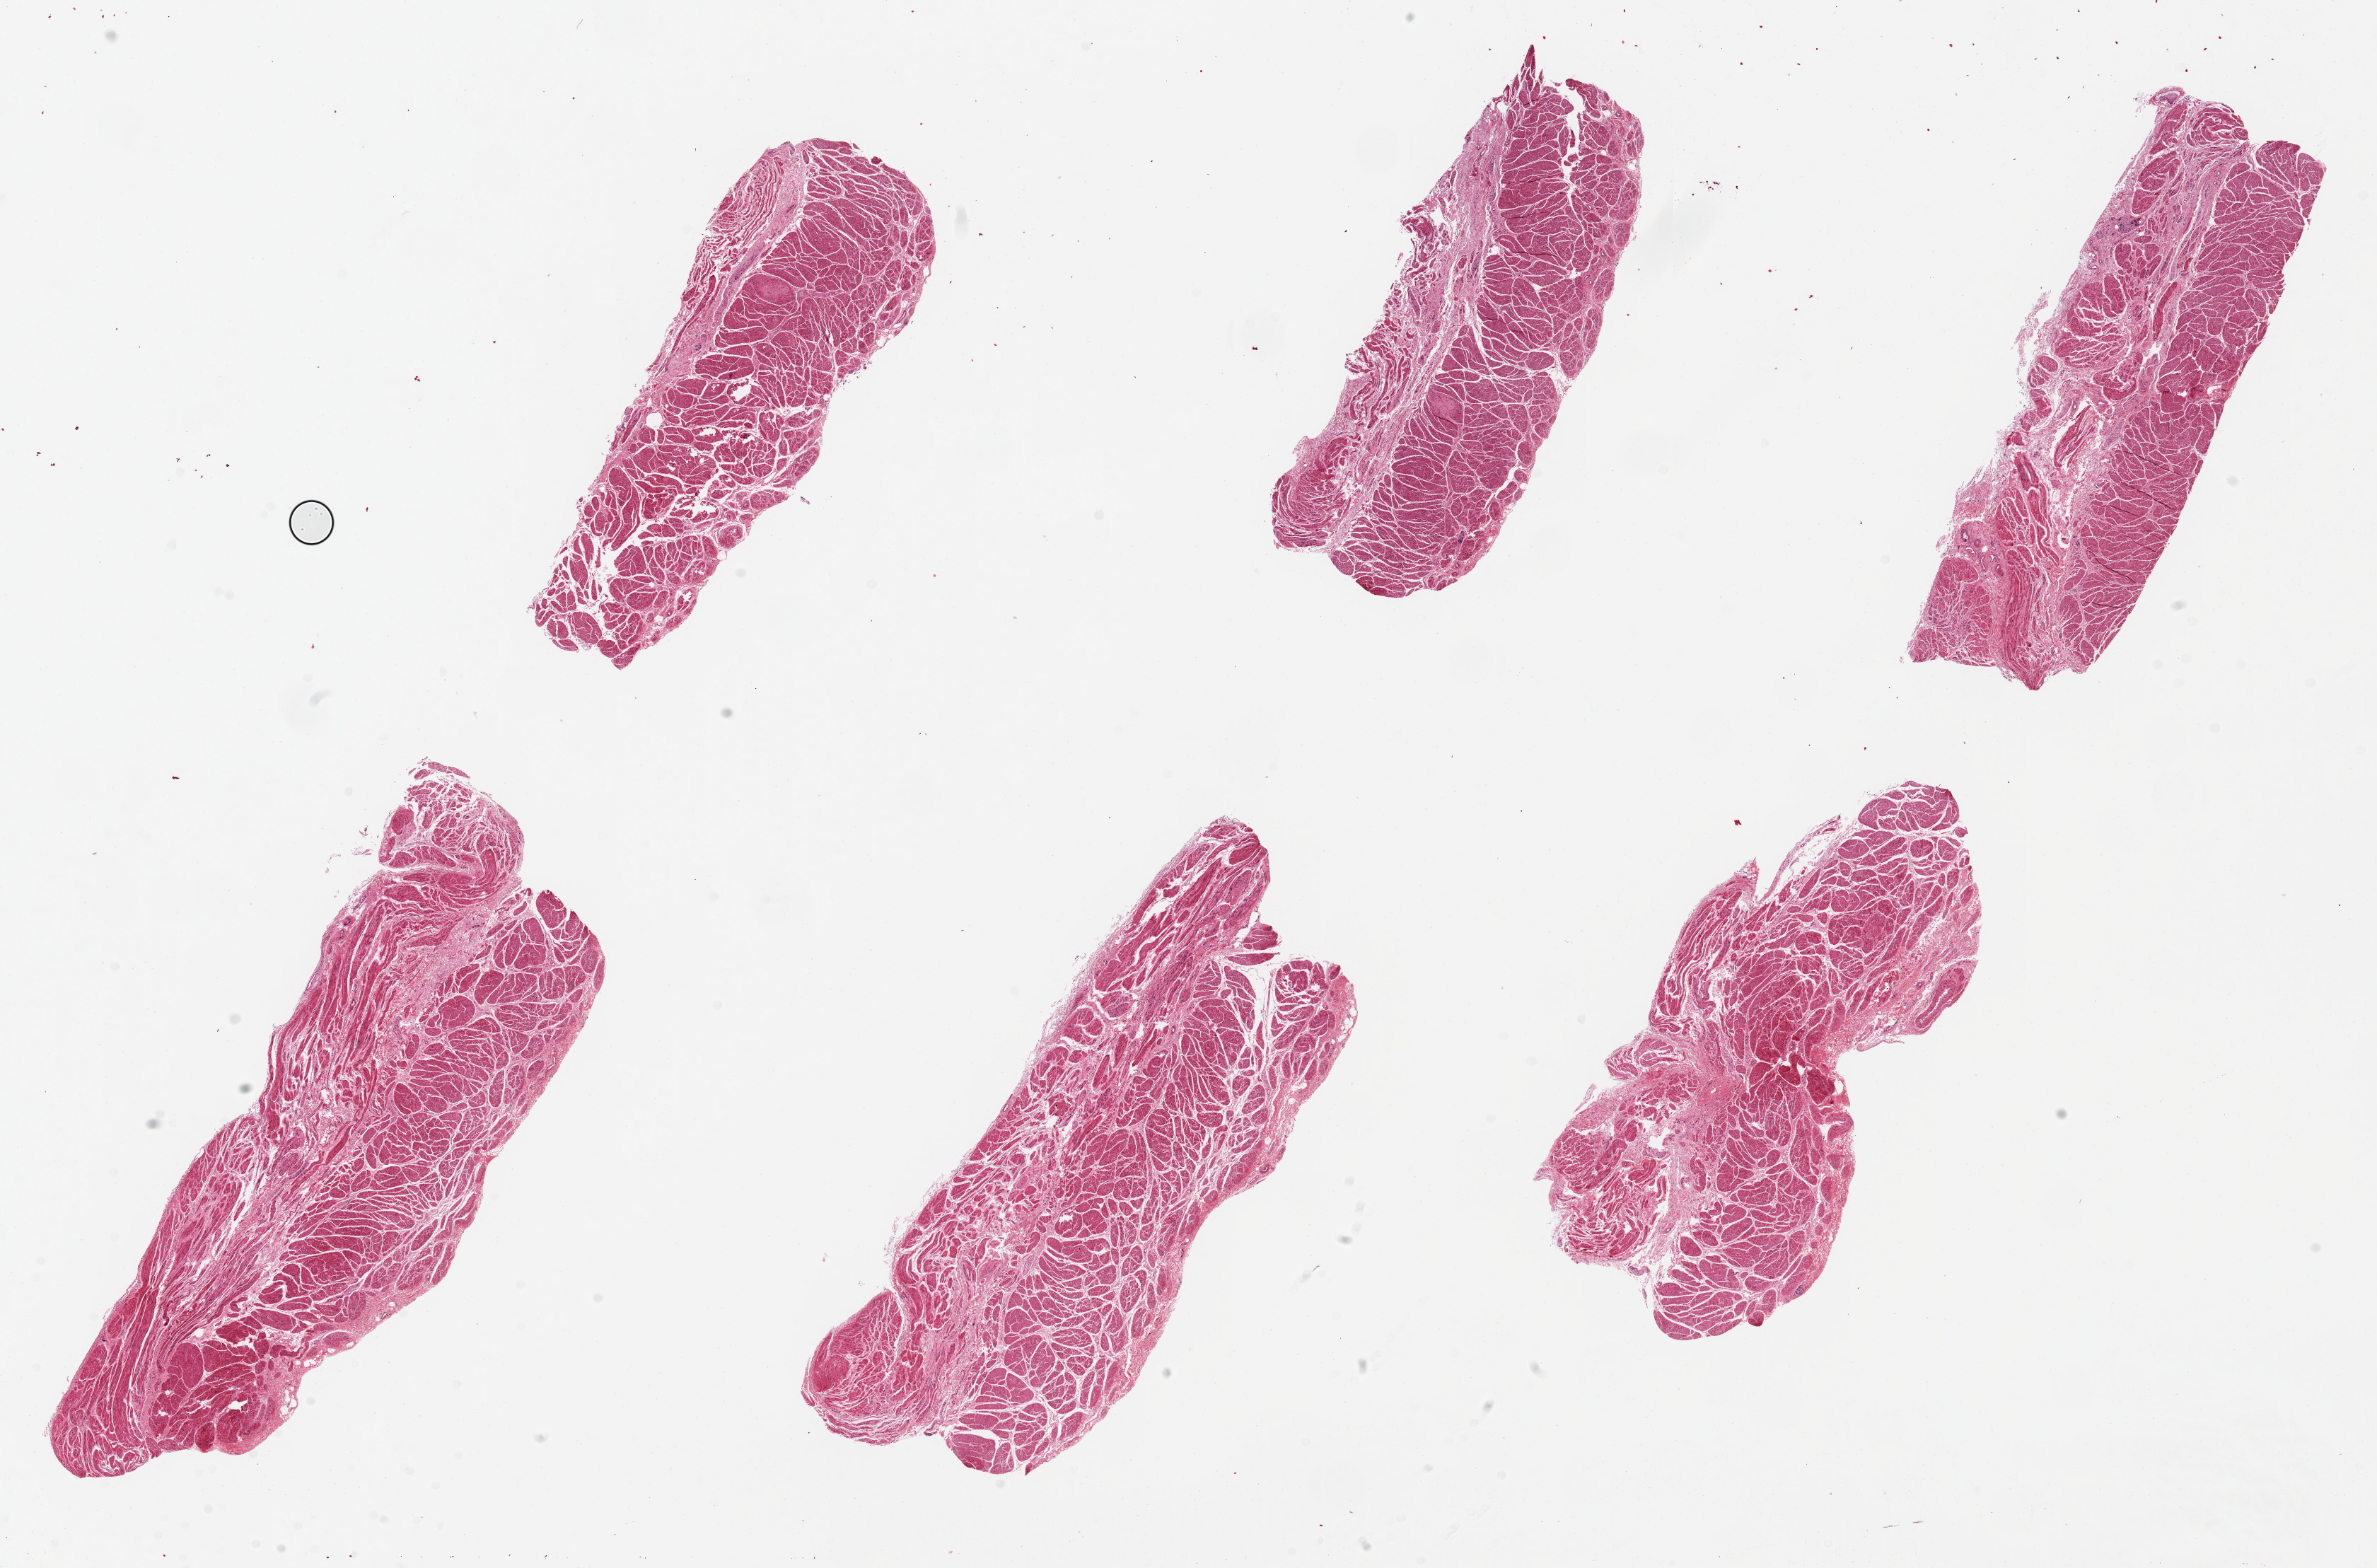
Whole-slide image, haematoxylin and eosin stain, low-resolution overview of the scanned area, about 26.6 x 17.5 mm (slide scanned at 20x); PAXgene-fixed paraffin-embedded (PFPE) section; sampled site (target tissue): gastroesophageal junction; tissue donor sample. Male donor.
Review note (as recorded): 6 pieces ~8x3mm, all muscularis, good specimens.